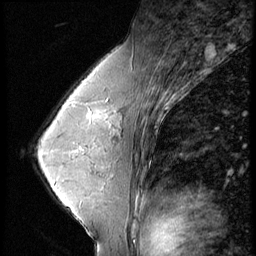
Breast MRI (dynamic contrast-enhanced), one sagittal slice; slice 39 of 56 in the series (ordered by position); 4 images stored at this slice position (order not interpretable as contrast timing); 1.5 T; TE 4.2 ms, TR 9 ms; 2.5 mm slice thickness; 256 × 256 image matrix, field of view 180 × 180 mm. Patient: female, 45 years. Case-level facts recorded for this patient, not image findings: setting: breast cancer imaged before/during neoadjuvant chemotherapy; receptor status: triple-negative.
Outlined on this slice (semi-automatically segmented with operator editing):
- analysis volume of interest (the breast-tissue region the enhancement analysis was run in; not a lesion): box from (x=77, y=104) to (x=97, y=124) px
- tumour enhancement mask (voxels above the 140 % enhancement threshold inside the analysis volume of interest): (x=83, y=104)–(x=97, y=123)